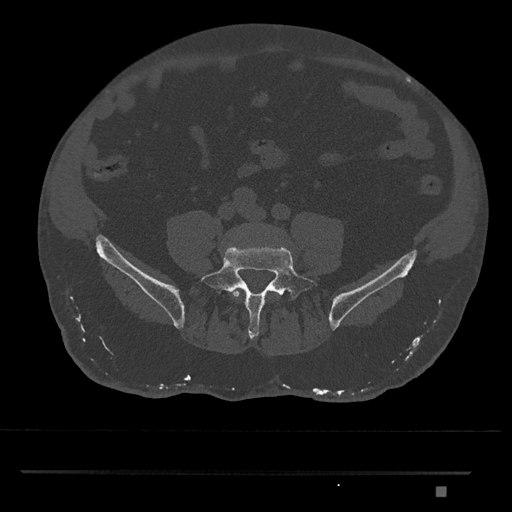
CT including the spine, one axial slice. Slice 566 of 1134 in the series (ordered by position). Reconstruction kernel Br40s/3. Bone window (W 1800 / L 400 HU). 0.5 mm slice thickness. 512 × 512 image matrix, field of view 429 × 429 mm. Patient: male, 65 years. From the clinical record (not read from this slice): primary cancer: prostate.
Outlined on this slice (semi-automatically segmented with operator editing):
- L4 vertebra: bounding box [x1, y1, x2, y2] px = [230, 290, 281, 299]
- L5 vertebra: [200, 246, 319, 339]